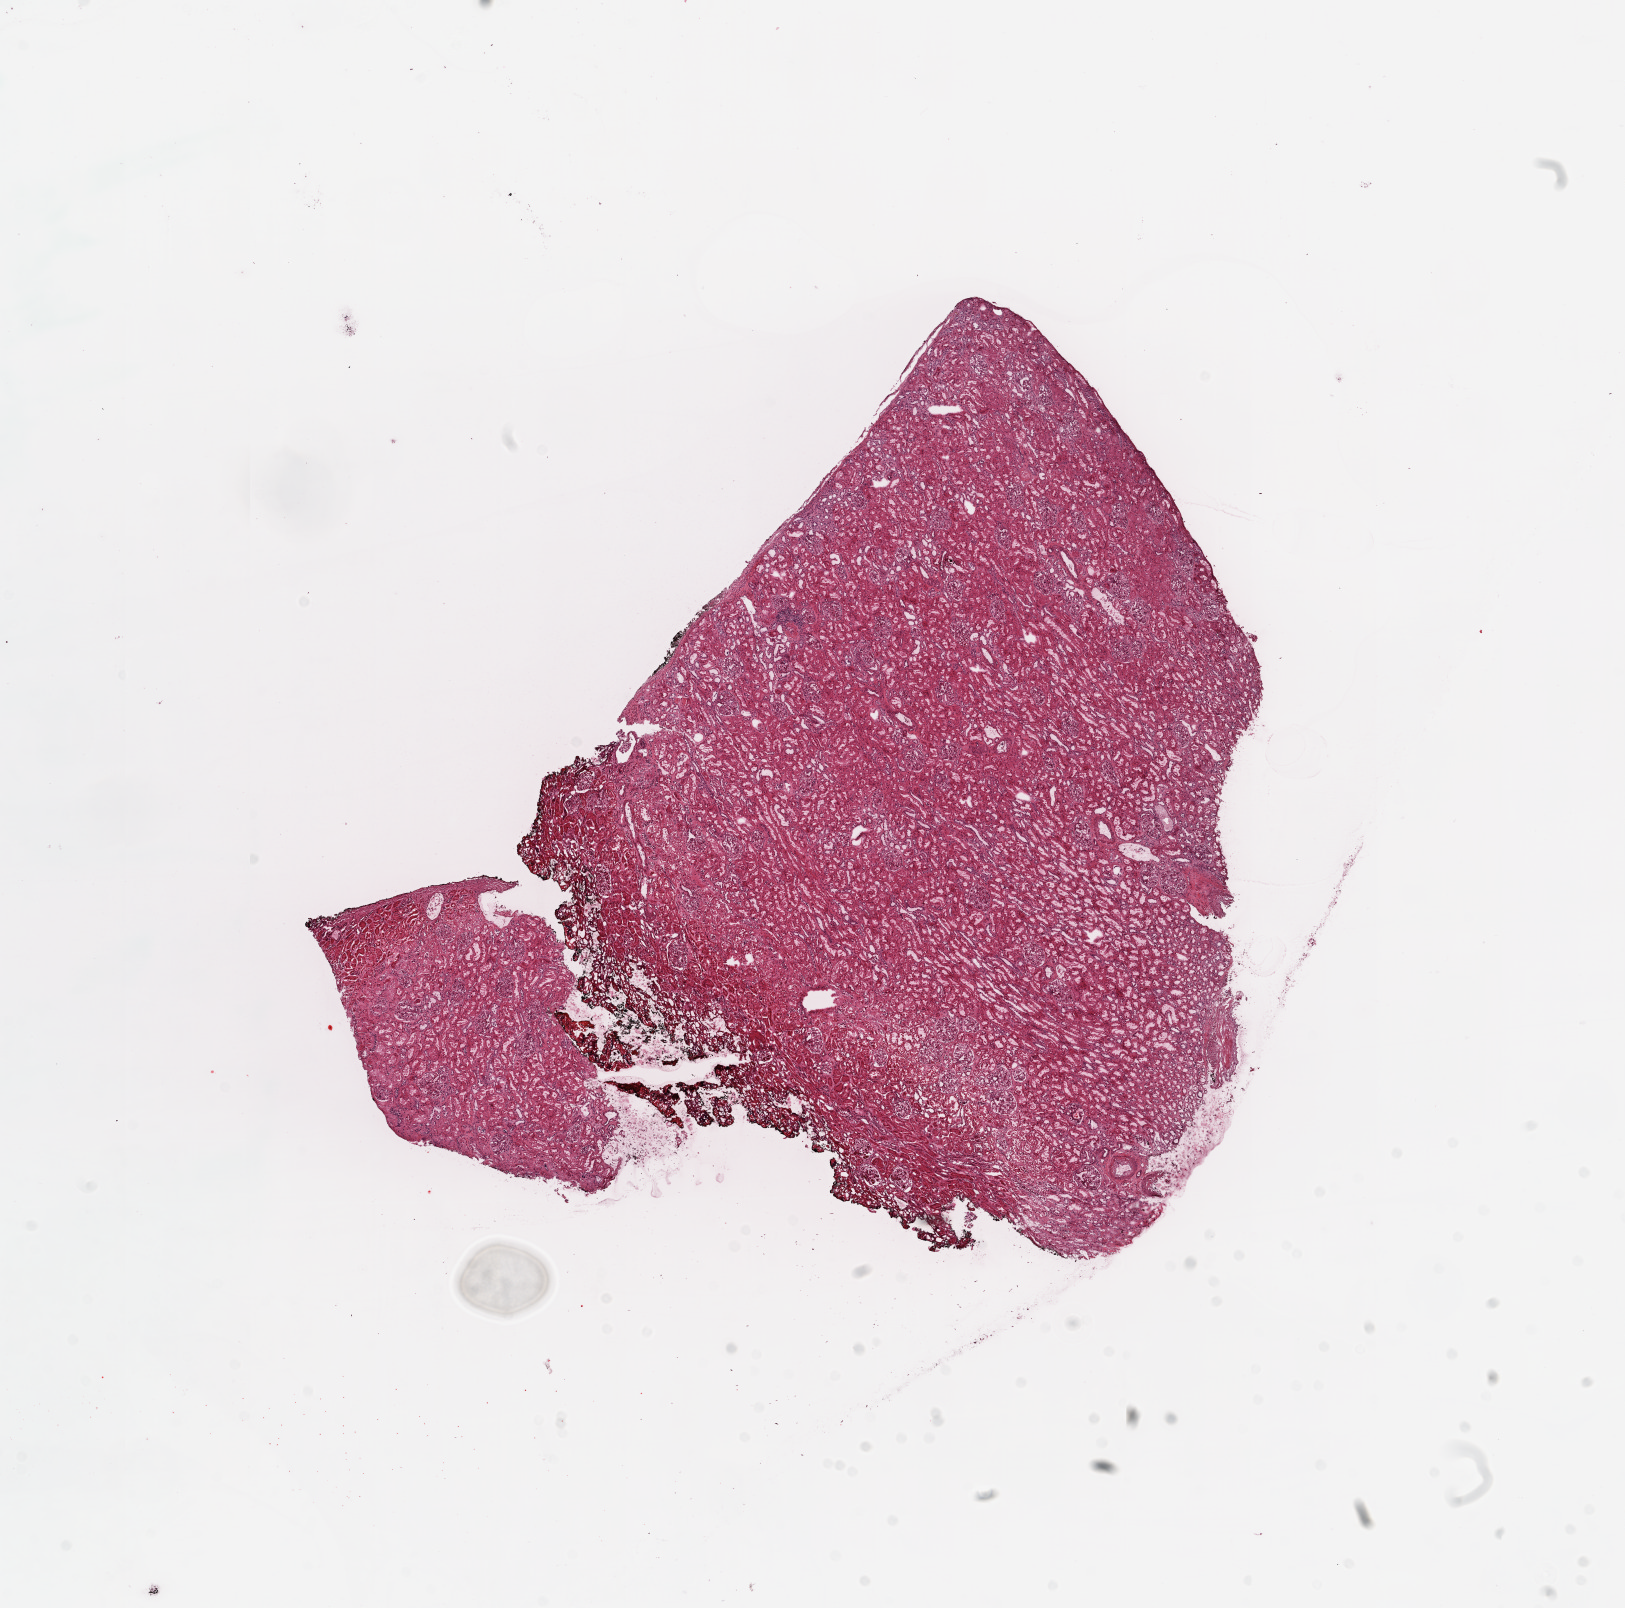
H&E-stained whole-slide image, whole scanned area (about 13.0 x 12.9 mm, slide scanned at 20x) shown as a low-resolution overview; frozen section from the top of the tissue portion; sample: solid tissue normal (non-tumour tissue), kidney. Male, age 42 years at initial diagnosis.
This section: solid tissue normal sample (biorepository sample class). Patient diagnosis: Clear cell adenocarcinoma, NOS.